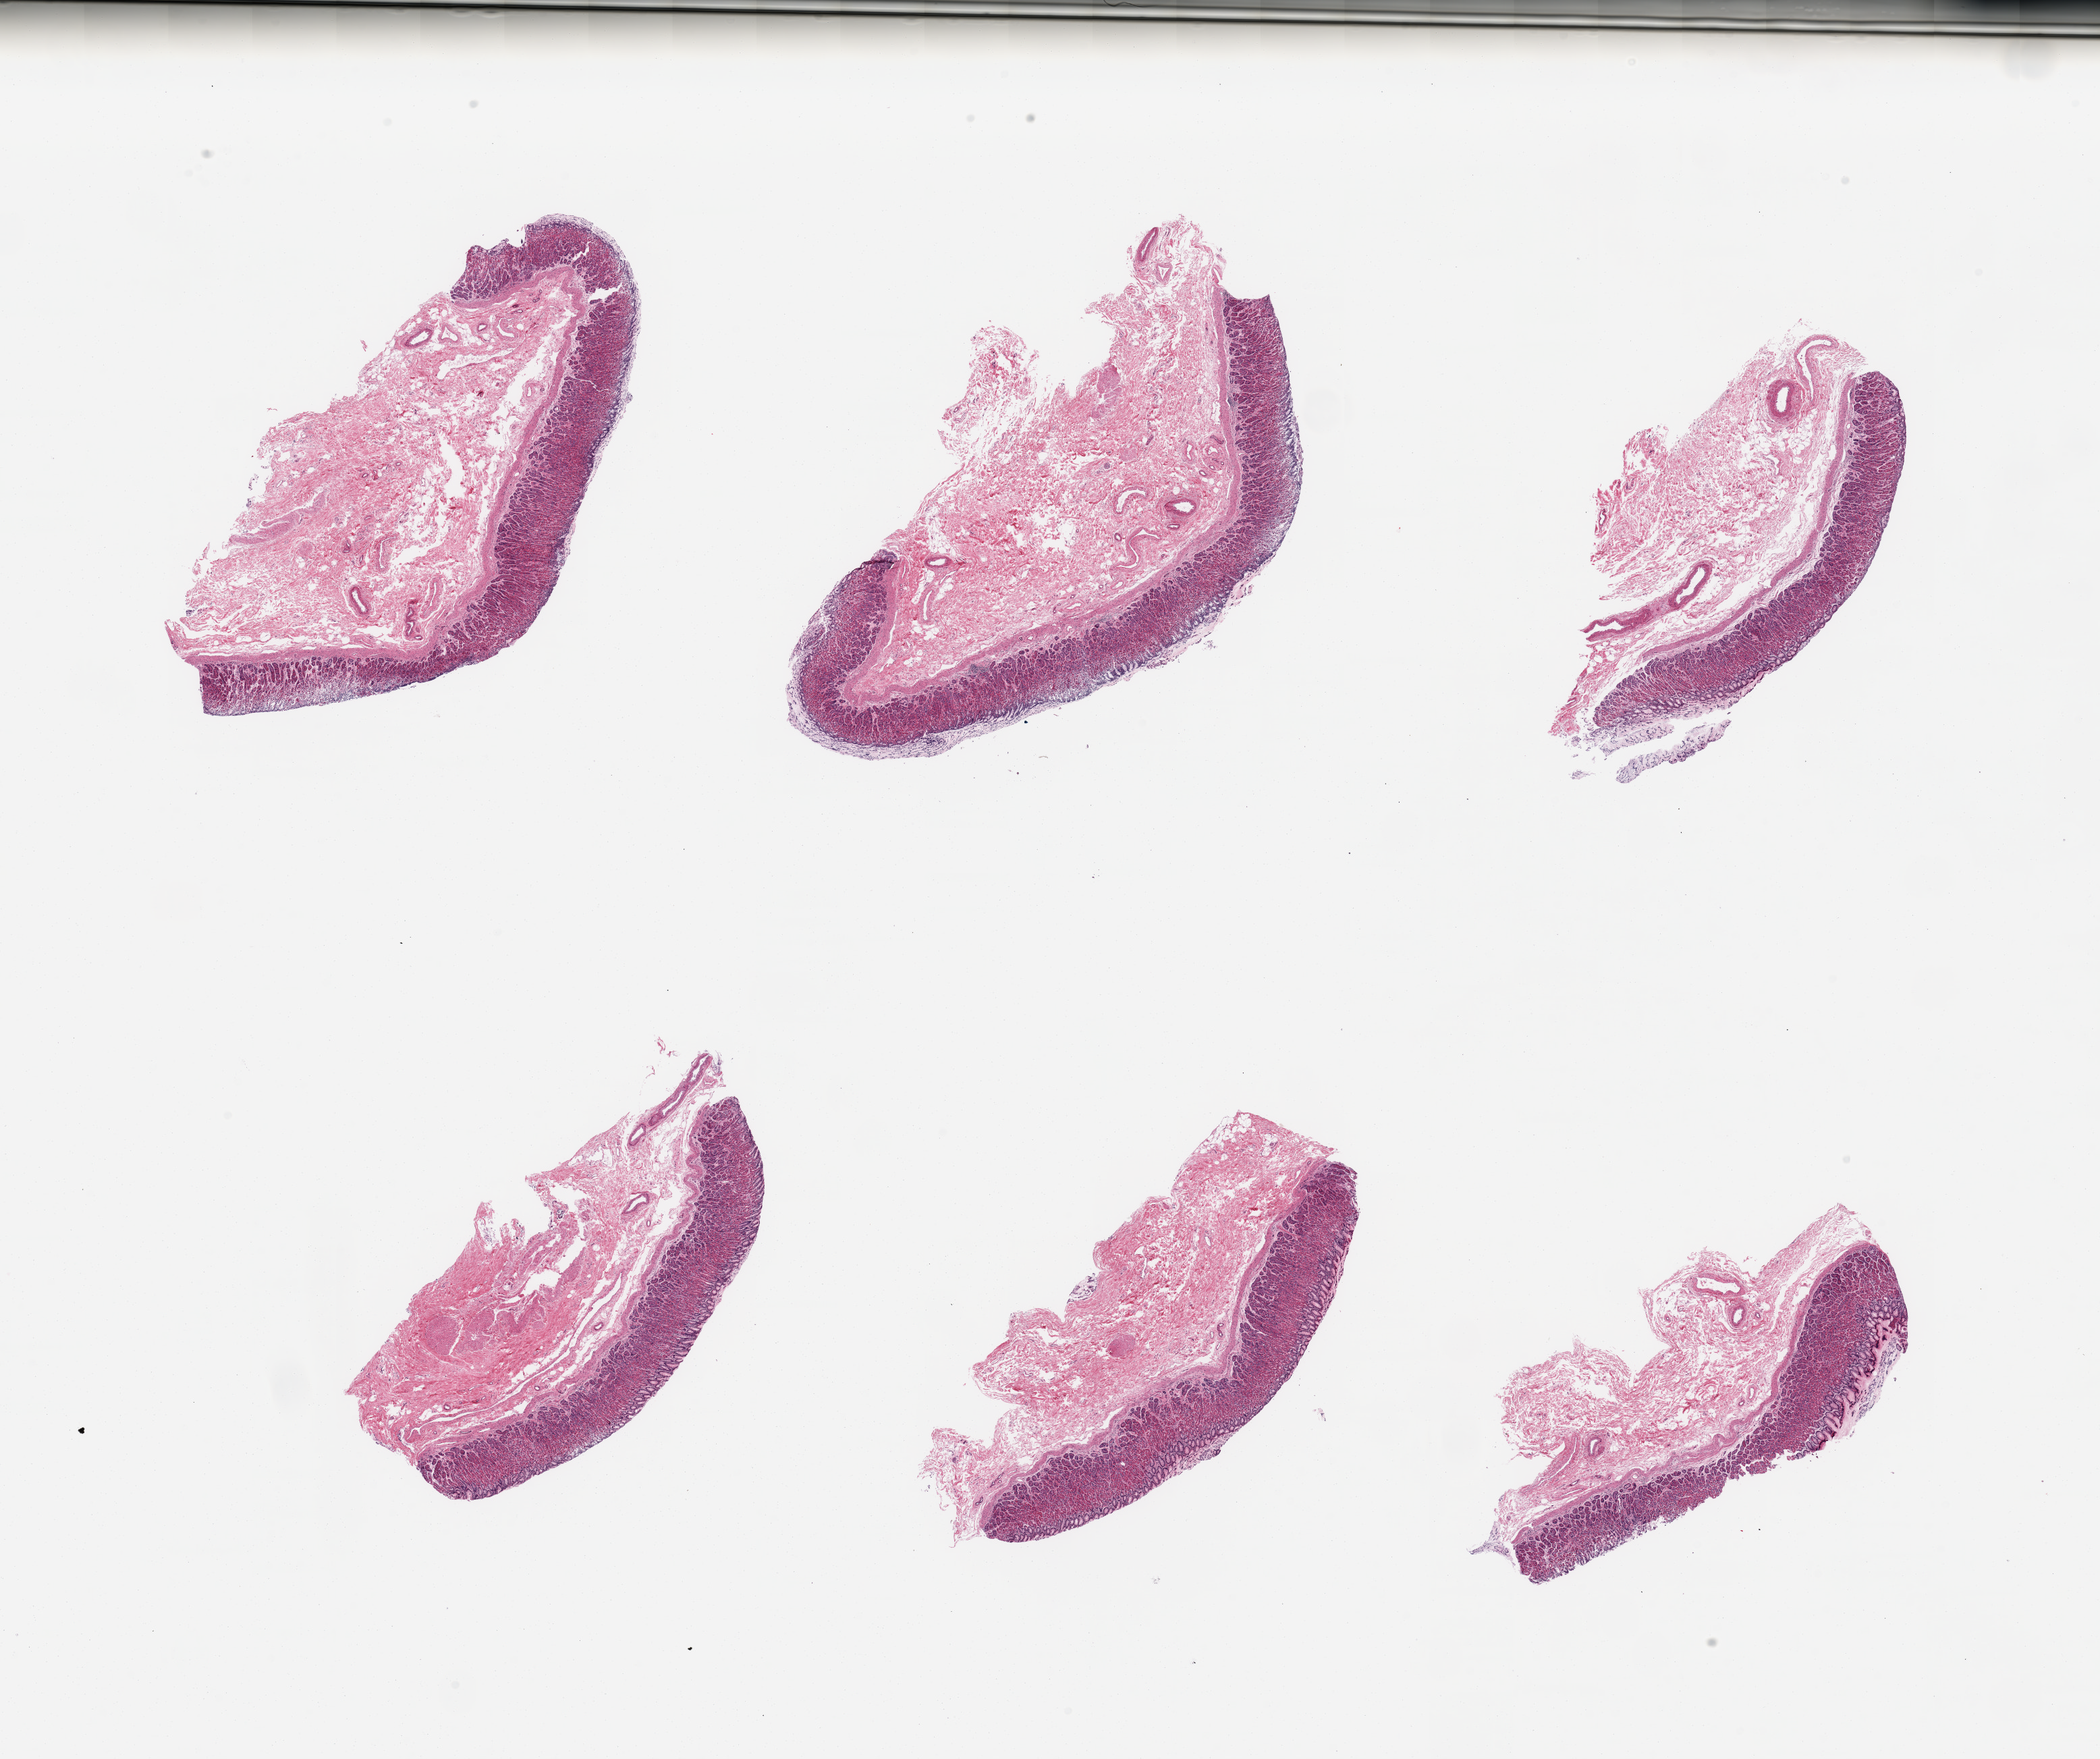
Digitized hematoxylin and eosin (H&E)-stained section, brightfield, shown as a low-resolution overview of the whole scanned area (about 24.6 x 20.6 mm, slide scanned at 20x); PAXgene-fixed paraffin-embedded (PFPE) section; sampled site (target tissue): stomach; donor tissue sample. Donor sex: female.
Review note (as recorded): 6 pieces; mildly to moderately autolyzed gastric mucosa.